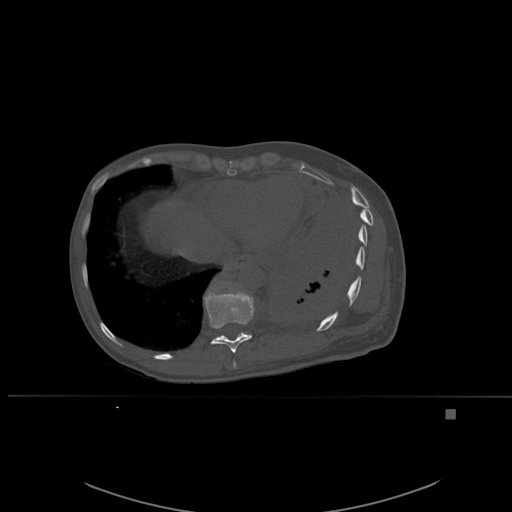
CT including the spine, one axial slice. Position 315 of 537 along the scan axis. Bone window (W 1800 / L 400 HU). 1.5 mm slice thickness. 512 × 512 image matrix, field of view 440 × 440 mm. Patient: female, 45 years. From the clinical record (not read from this slice): primary cancer: lung.
Annotated regions visible in this slice (semi-automatically segmented with operator editing):
- T10 vertebra: bounding box (x1, y1, x2, y2) in pixels: (204, 284, 255, 353)
- T11 vertebra: (214, 282, 248, 340)
- T9 vertebra: (233, 360, 237, 368)